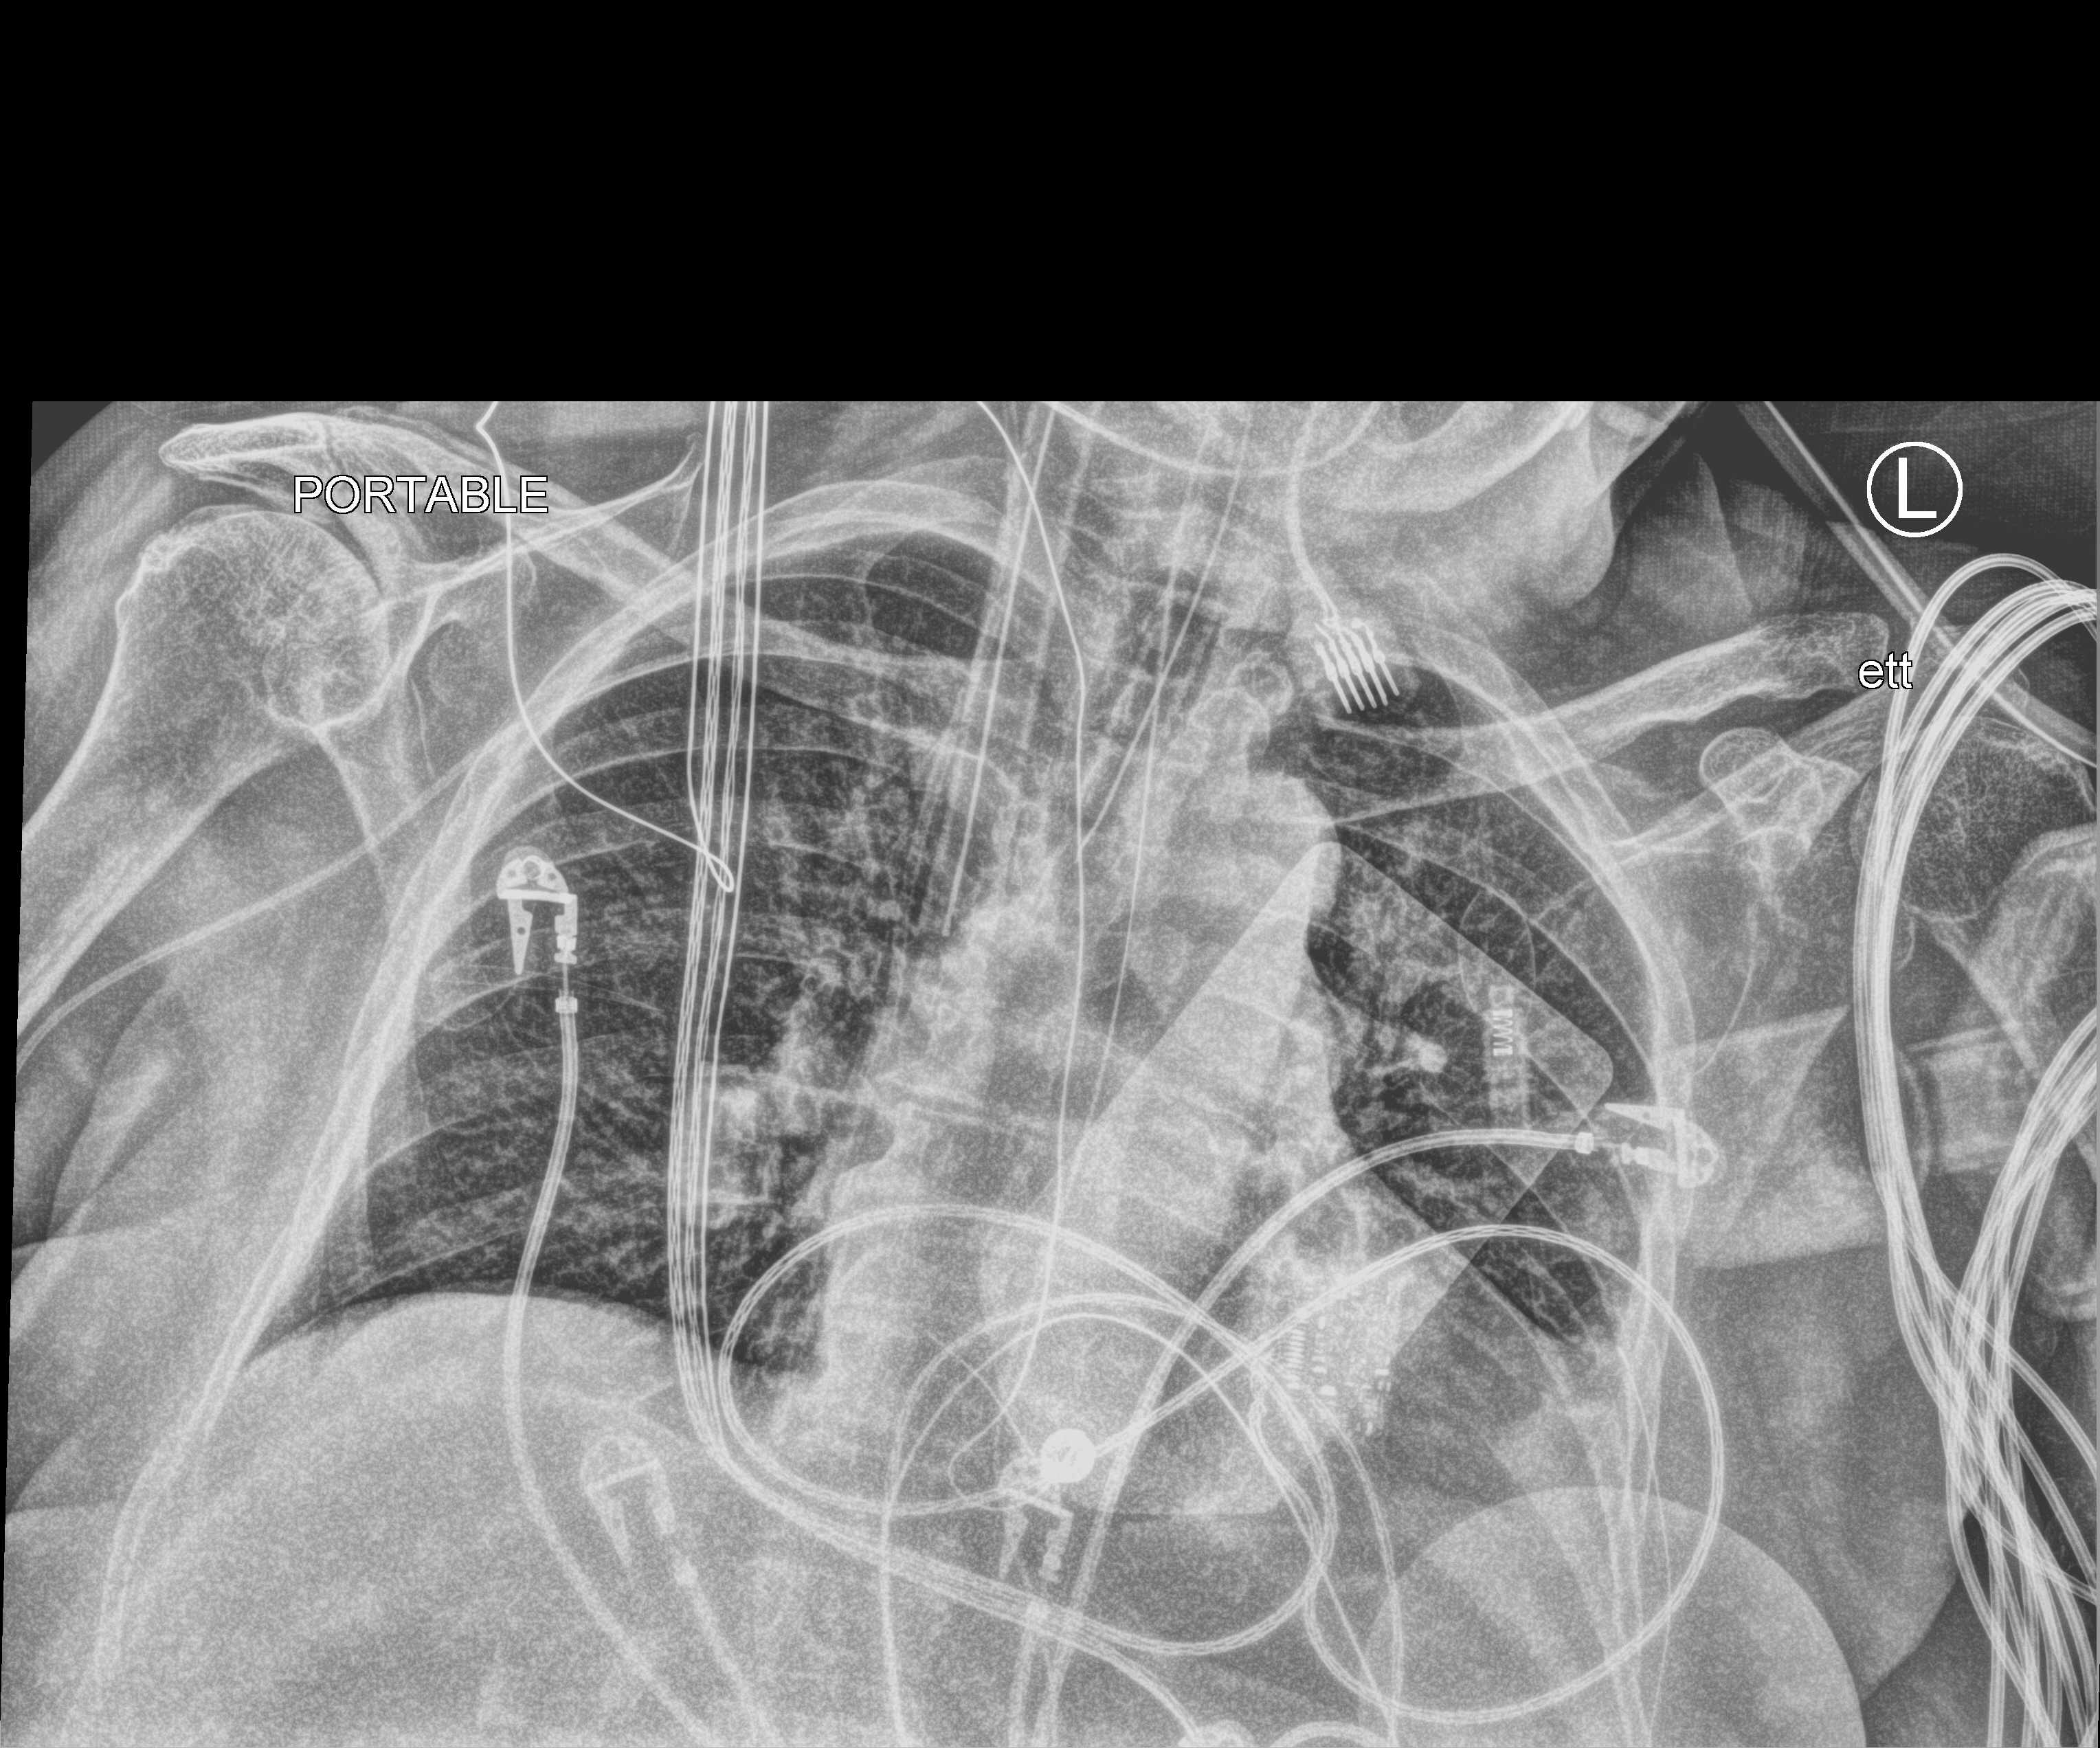
Portable chest radiograph; anteroposterior (AP) projection. Female patient hospitalised with COVID-19, age 75–90 years.
From the hospital-stay record, not from the radiograph (when in the stay this image was taken is not recorded): mechanically ventilated during this hospital stay: yes; admitted to intensive care during this hospital stay: yes.